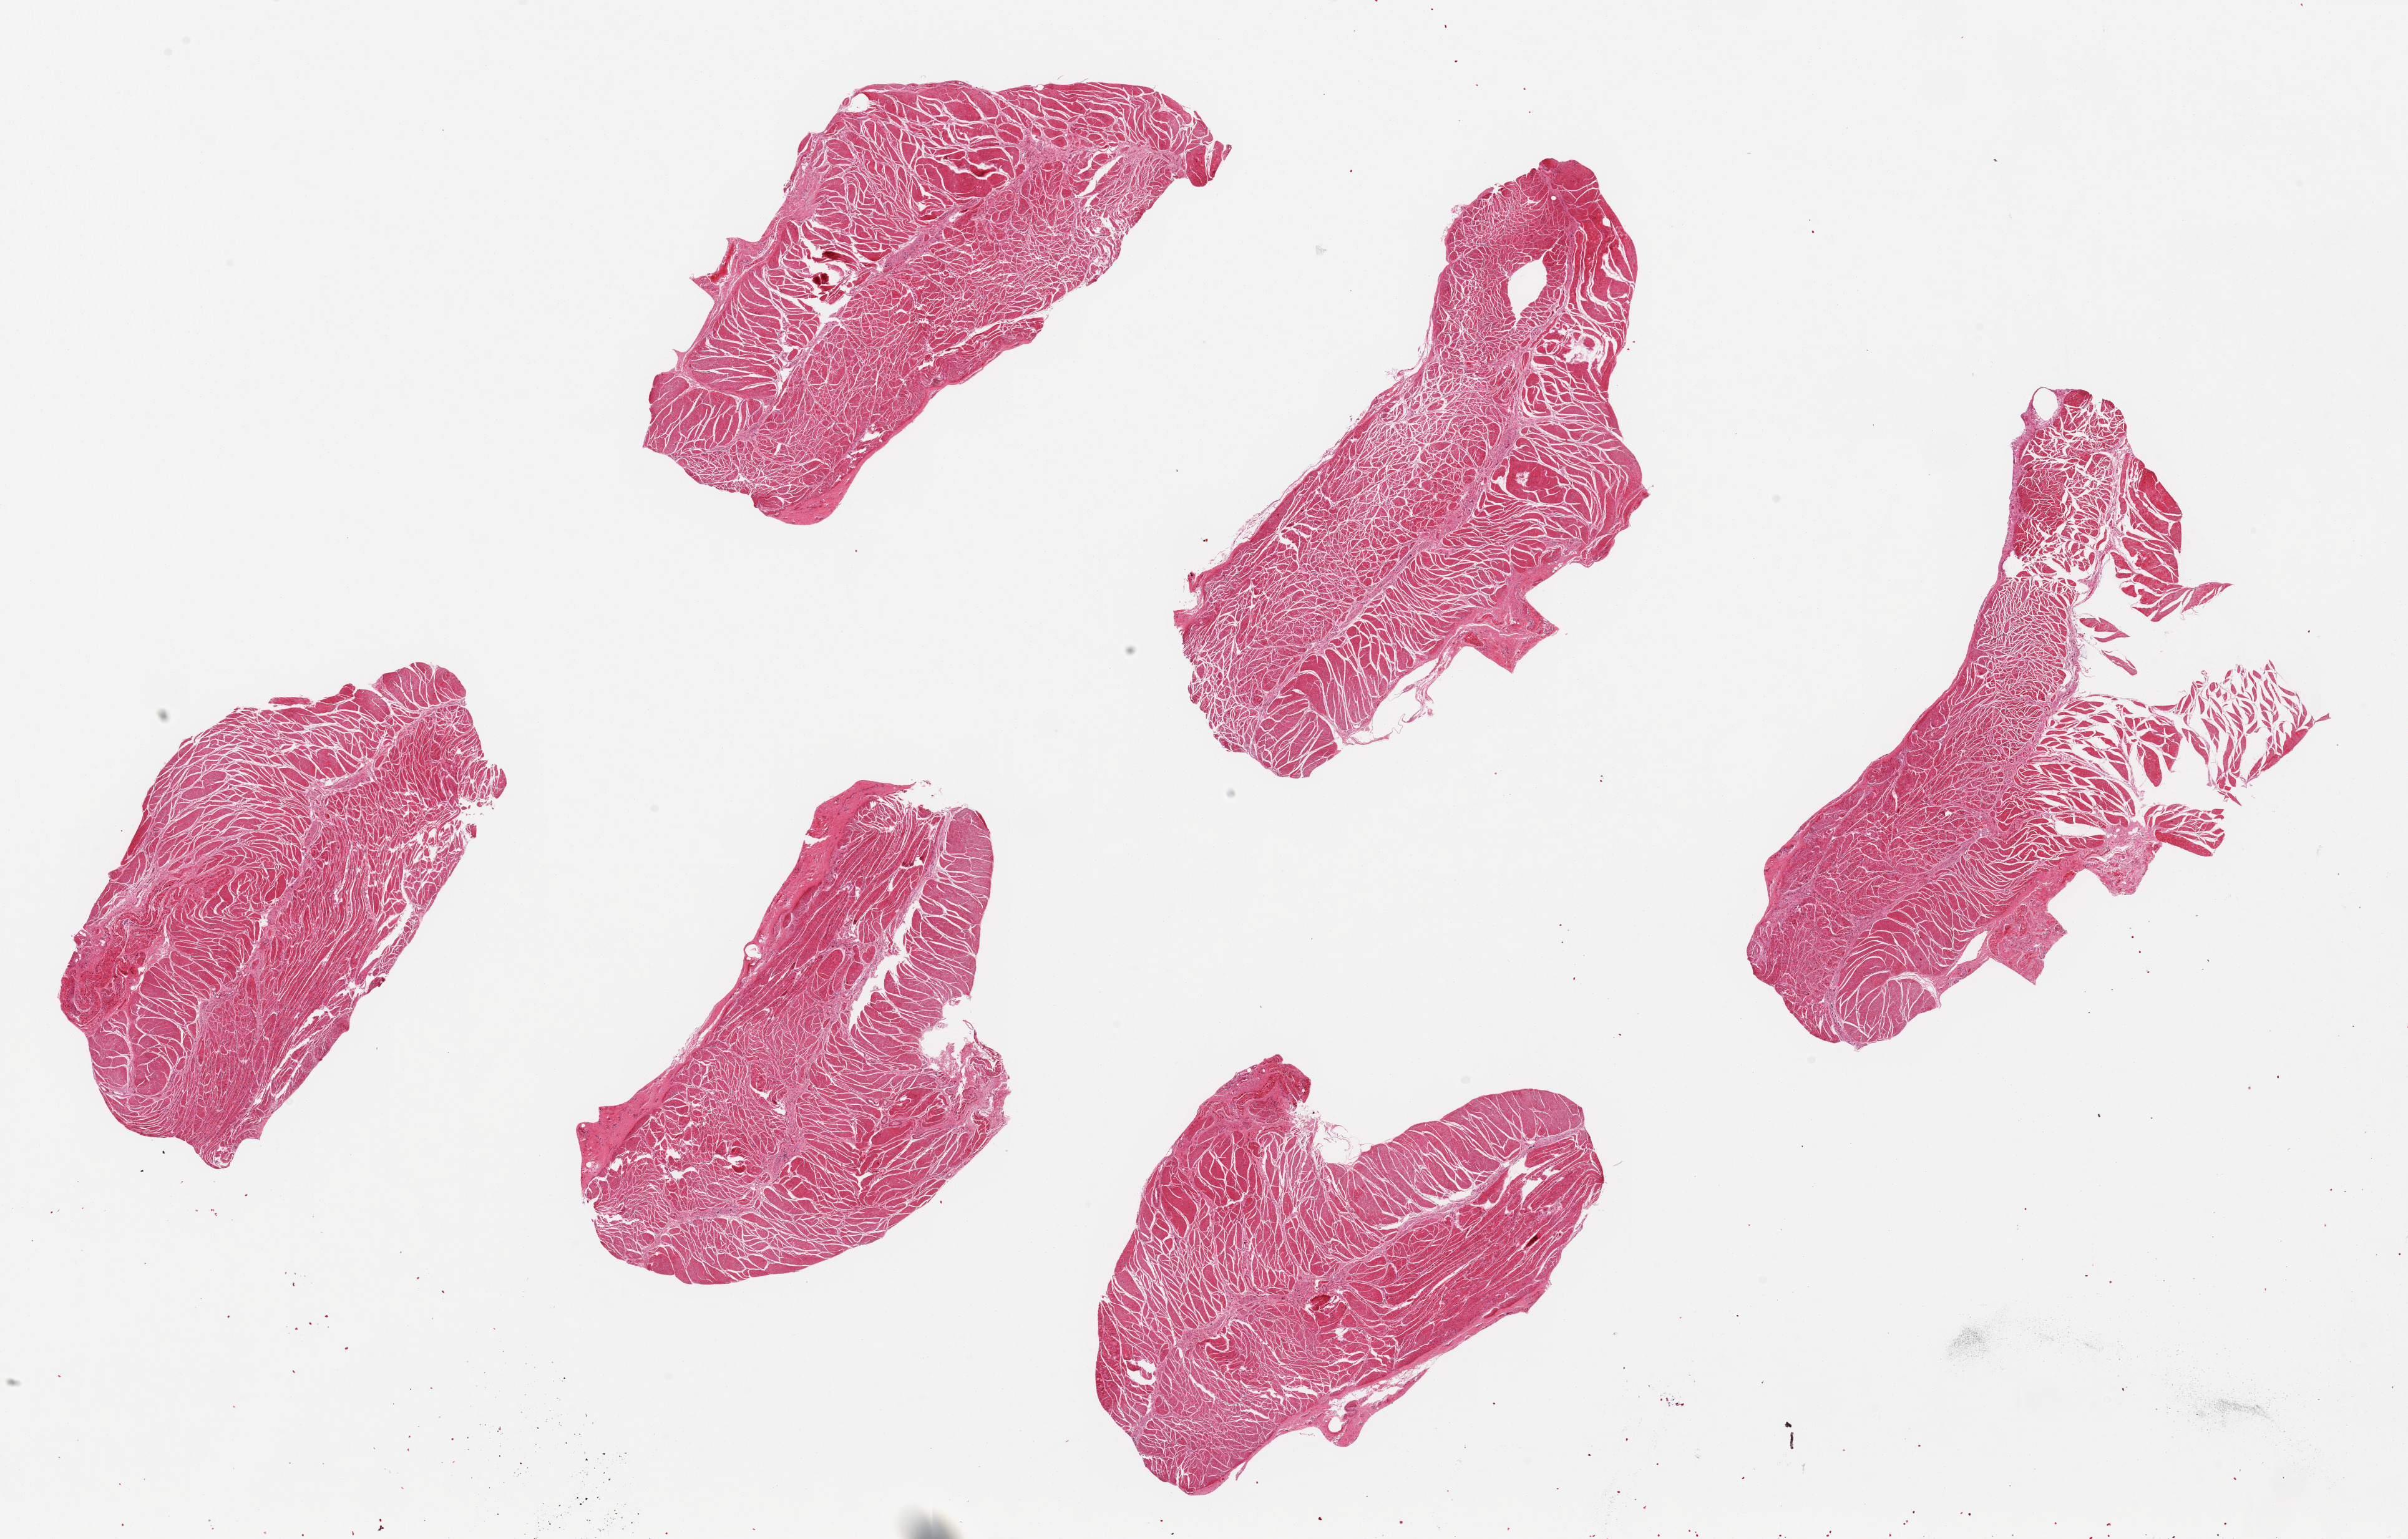
Whole-slide image, H&E stain, brightfield, a low-resolution overview of the entire scanned area, about 30.5 x 19.5 mm (acquisition: 20x scan). PAXgene-fixed, paraffin-embedded tissue. Section of esophageal muscle (target tissue). Donor tissue sample. Donor: female.
Reviewer comment on this tissue sample: 6 pieces up to 7x4 mm.